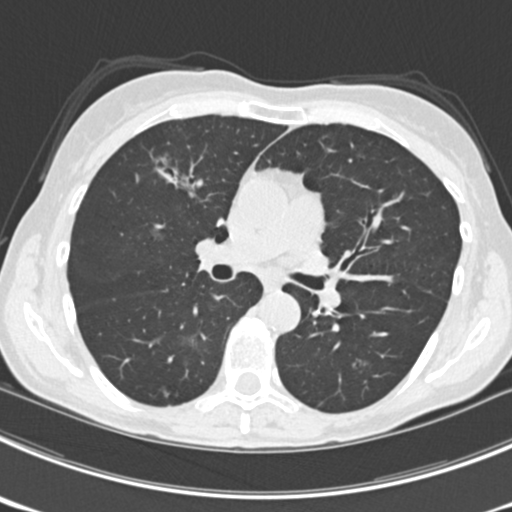
Chest CT (low-dose screening protocol), one axial image. Third annual screen. Lung window (W 1500 / L -600 HU). 2 mm slice thickness. Standard (soft-tissue) reconstruction kernel (B30f). 120 kVp. Slice 88 of 225 in the series. Female, age 63 years at enrolment.
- Lesion marked by an expert reader, box from (x=149, y=146) to (x=212, y=203) px.
- The screening reader recorded 9 non-calcified nodules or masses ≥4 mm on this exam (left upper lobe, right upper lobe, left upper lobe, left lower lobe, right middle lobe, left lower lobe, left lower lobe, right lower lobe, right lower lobe); which of them this box marks is not recorded.
- Official screen result: positive, other.
- Participant outcome: lung cancer diagnosed 15 days after this screen — bronchiolo-alveolar adenocarcinoma, NOS, right upper lobe, right middle lobe, right lower lobe, left upper lobe, left lower lobe, moderately differentiated (G2), stage IV (AJCC 6th edition).